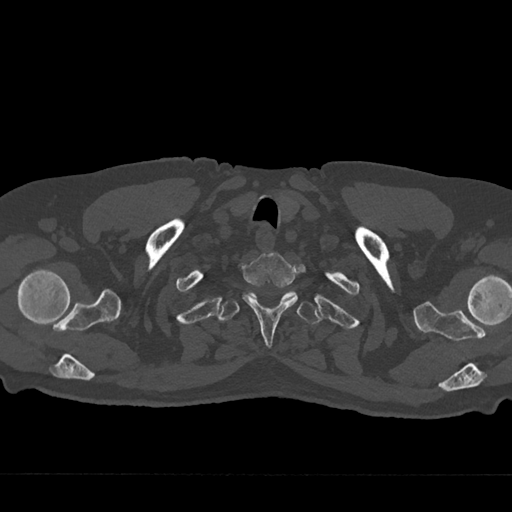
CT including the spine, one axial slice. Slice 644 of 797 in the series (ordered by position). Reconstruction kernel Br40s/3. 120 kVp. Bone window (W 1800 / L 400 HU). 0.5 mm slice thickness. 512 × 512 image matrix, field of view 377 × 377 mm. Patient: male, 75 years. From the clinical record (not read from this slice): primary cancer: renal; vertebrae with lytic lesions (as recorded): T4.
Outlined on this slice (semi-automatic segmentation, software-assisted and operator-edited):
- T1 vertebra: box from (x=242, y=253) to (x=298, y=348) px
- T2 vertebra: (x=218, y=290)–(x=321, y=325)